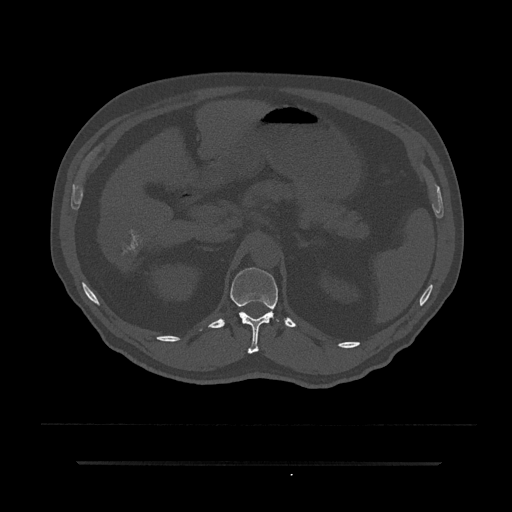
CT including the spine, one axial slice; position 203 of 797 along the scan axis; reconstruction kernel Br40s/3; 120 kVp; bone window (W 1800 / L 400 HU); 0.5 mm slice thickness; 512 × 512 image matrix, field of view 464 × 464 mm. Male patient, age 59 years. Case-level facts recorded for this patient, not image findings: primary cancer: bile ducts; vertebrae with lytic lesions (as recorded): T10.
Annotated regions visible in this slice (semi-automatically segmented with operator editing):
- T12 vertebra: bounding box [x1, y1, x2, y2] px = [230, 267, 280, 354]